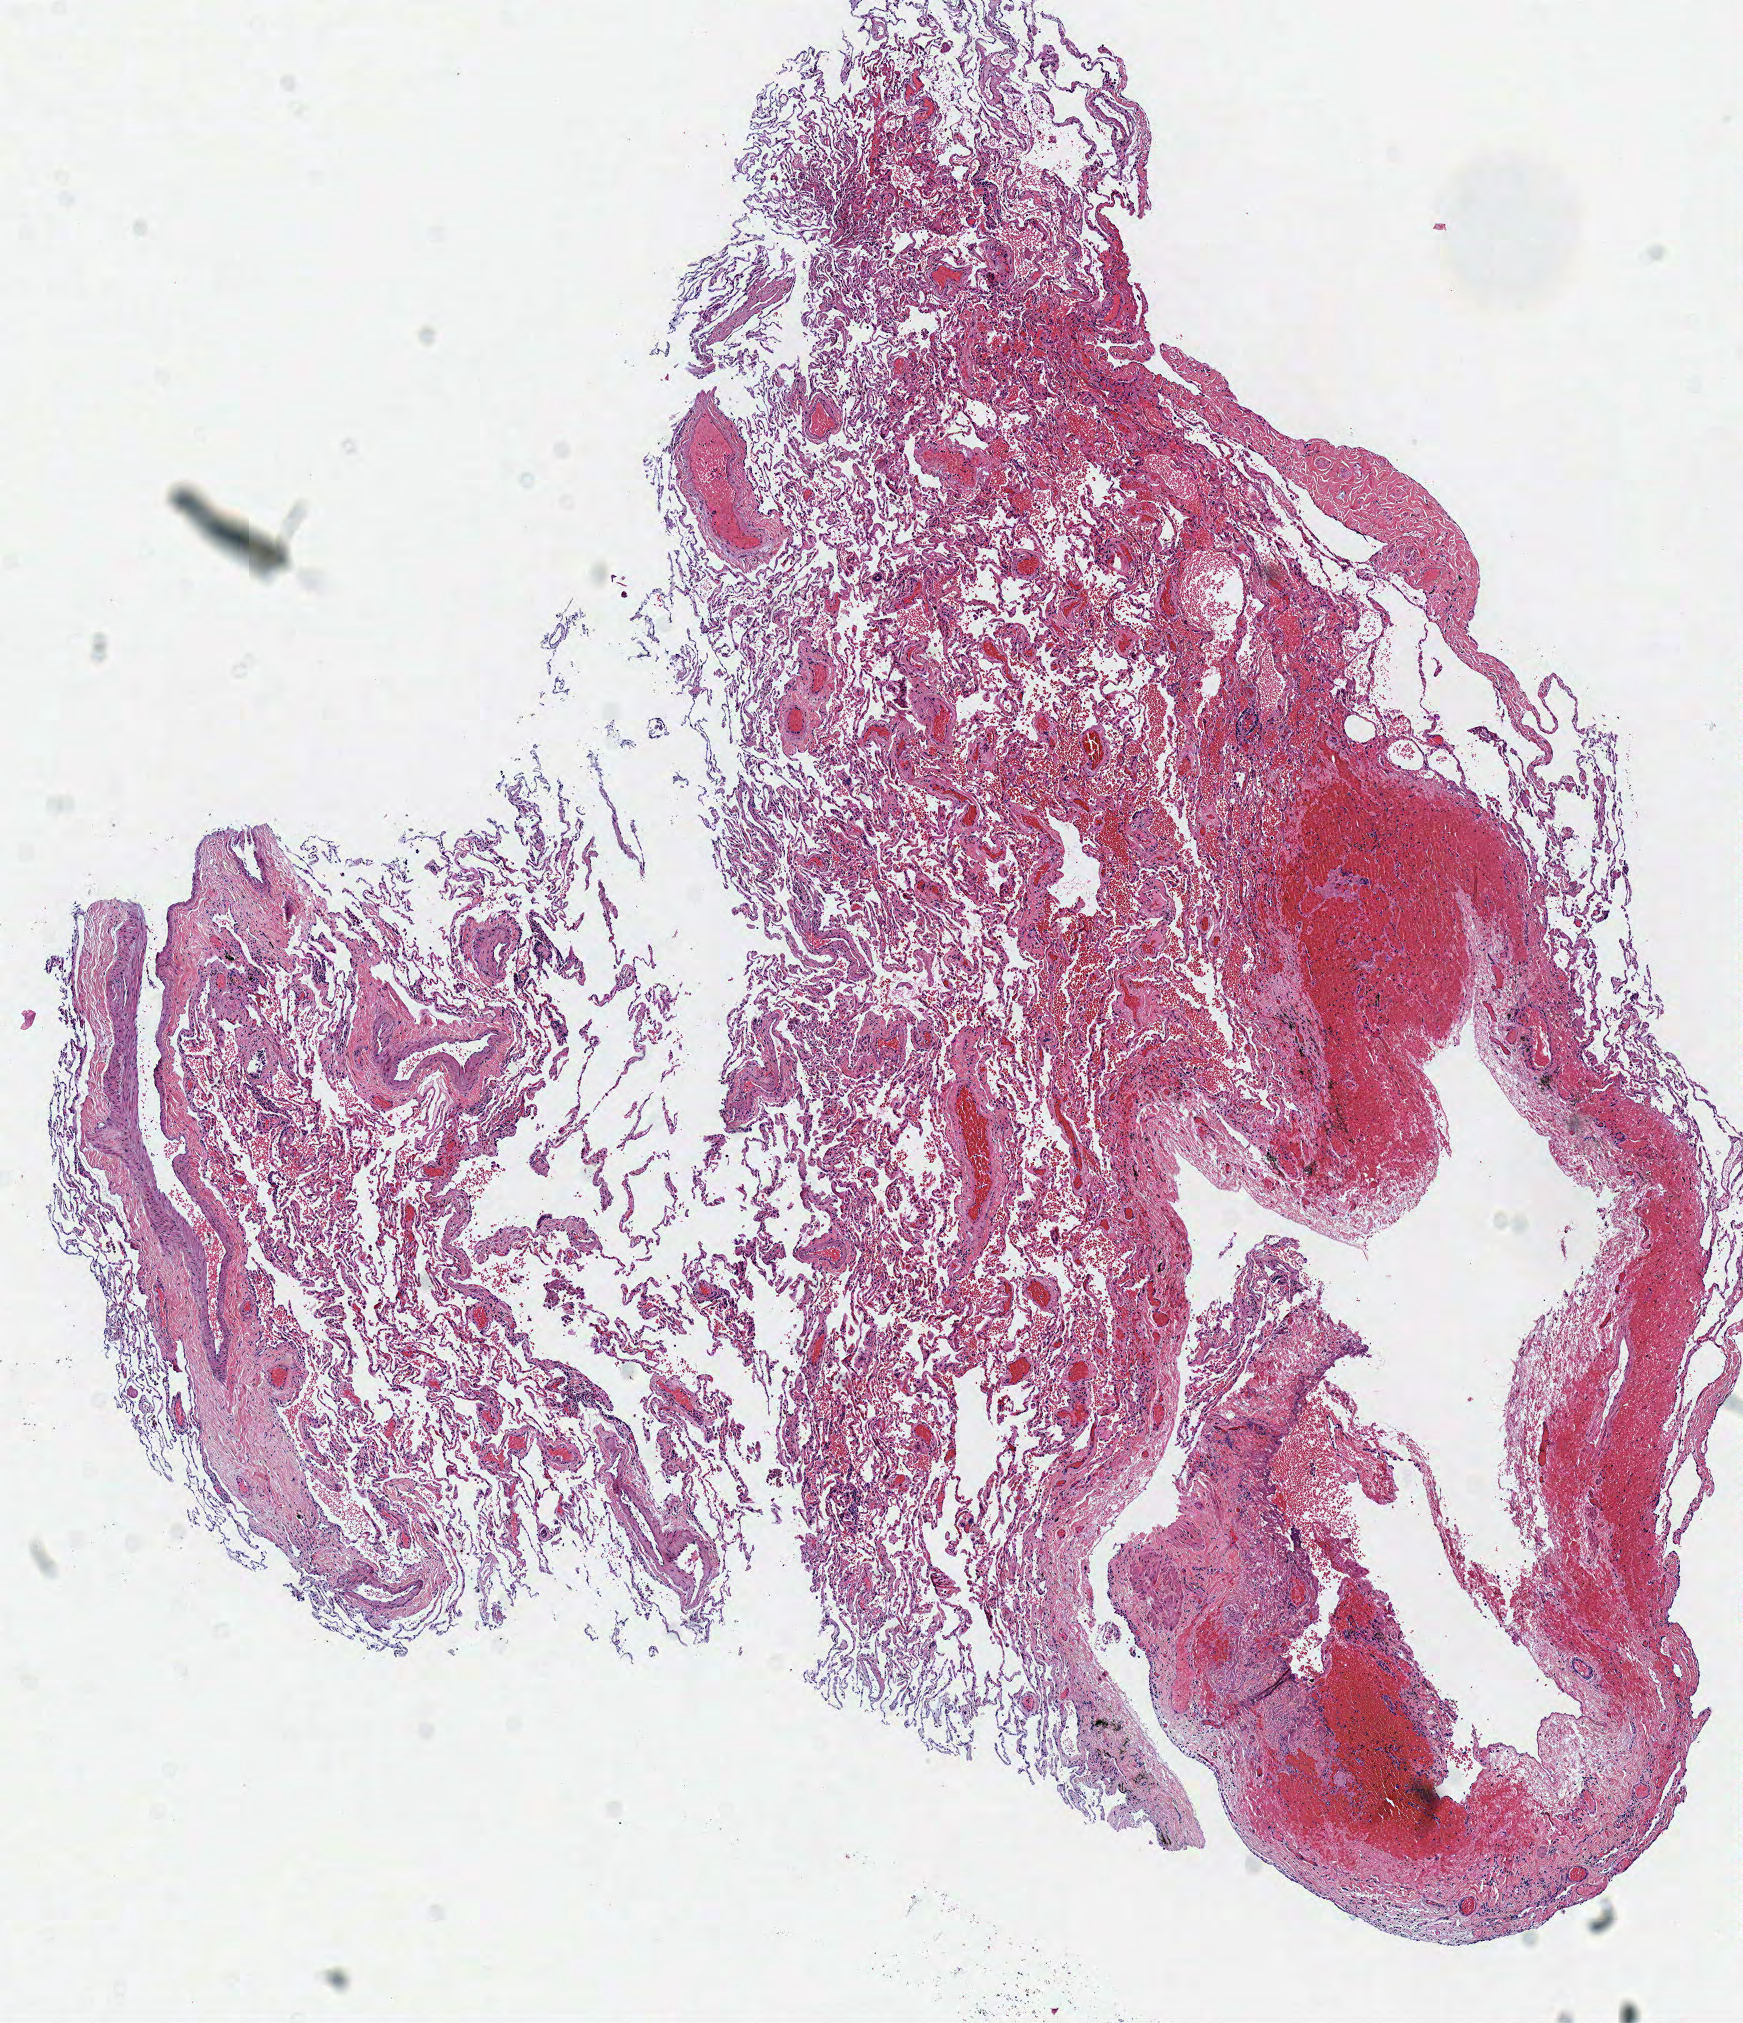
Whole-slide histology image, H&E — a low-resolution overview of the entire scanned area, about 6.9 x 8.0 mm (from a 40x scan), frozen section from the top of the tissue portion, sample: solid tissue normal (non-tumour tissue), lung. Male, age 59 years at initial diagnosis.
This section: solid tissue normal sample (biorepository sample class). Patient diagnosis: Adenocarcinoma, NOS.